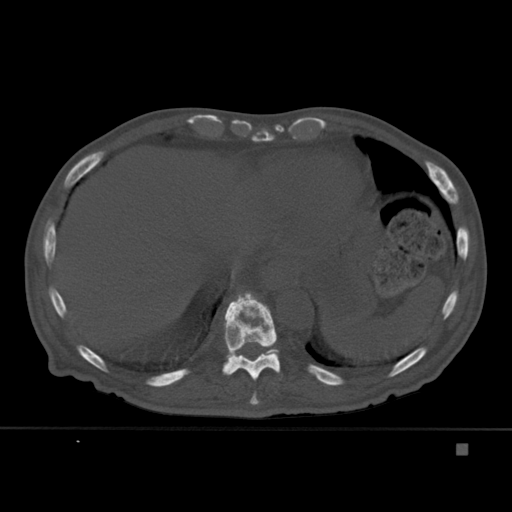
CT including the spine, one axial slice. Position 232 of 451 along the scan axis. Bone window (W 1800 / L 400 HU). 1.5 mm slice thickness. 512 × 512 image matrix, field of view 378 × 378 mm. Patient: male, 75 years. From the clinical record (not read from this slice): primary cancer: prostate.
Annotated regions visible in this slice (semi-automatic segmentation, software-assisted and operator-edited):
- T10 vertebra: bounding box (x1, y1, x2, y2) in pixels: (222, 291, 281, 381)
- T11 vertebra: (229, 349, 279, 356)
- T9 vertebra: (249, 391, 260, 405)